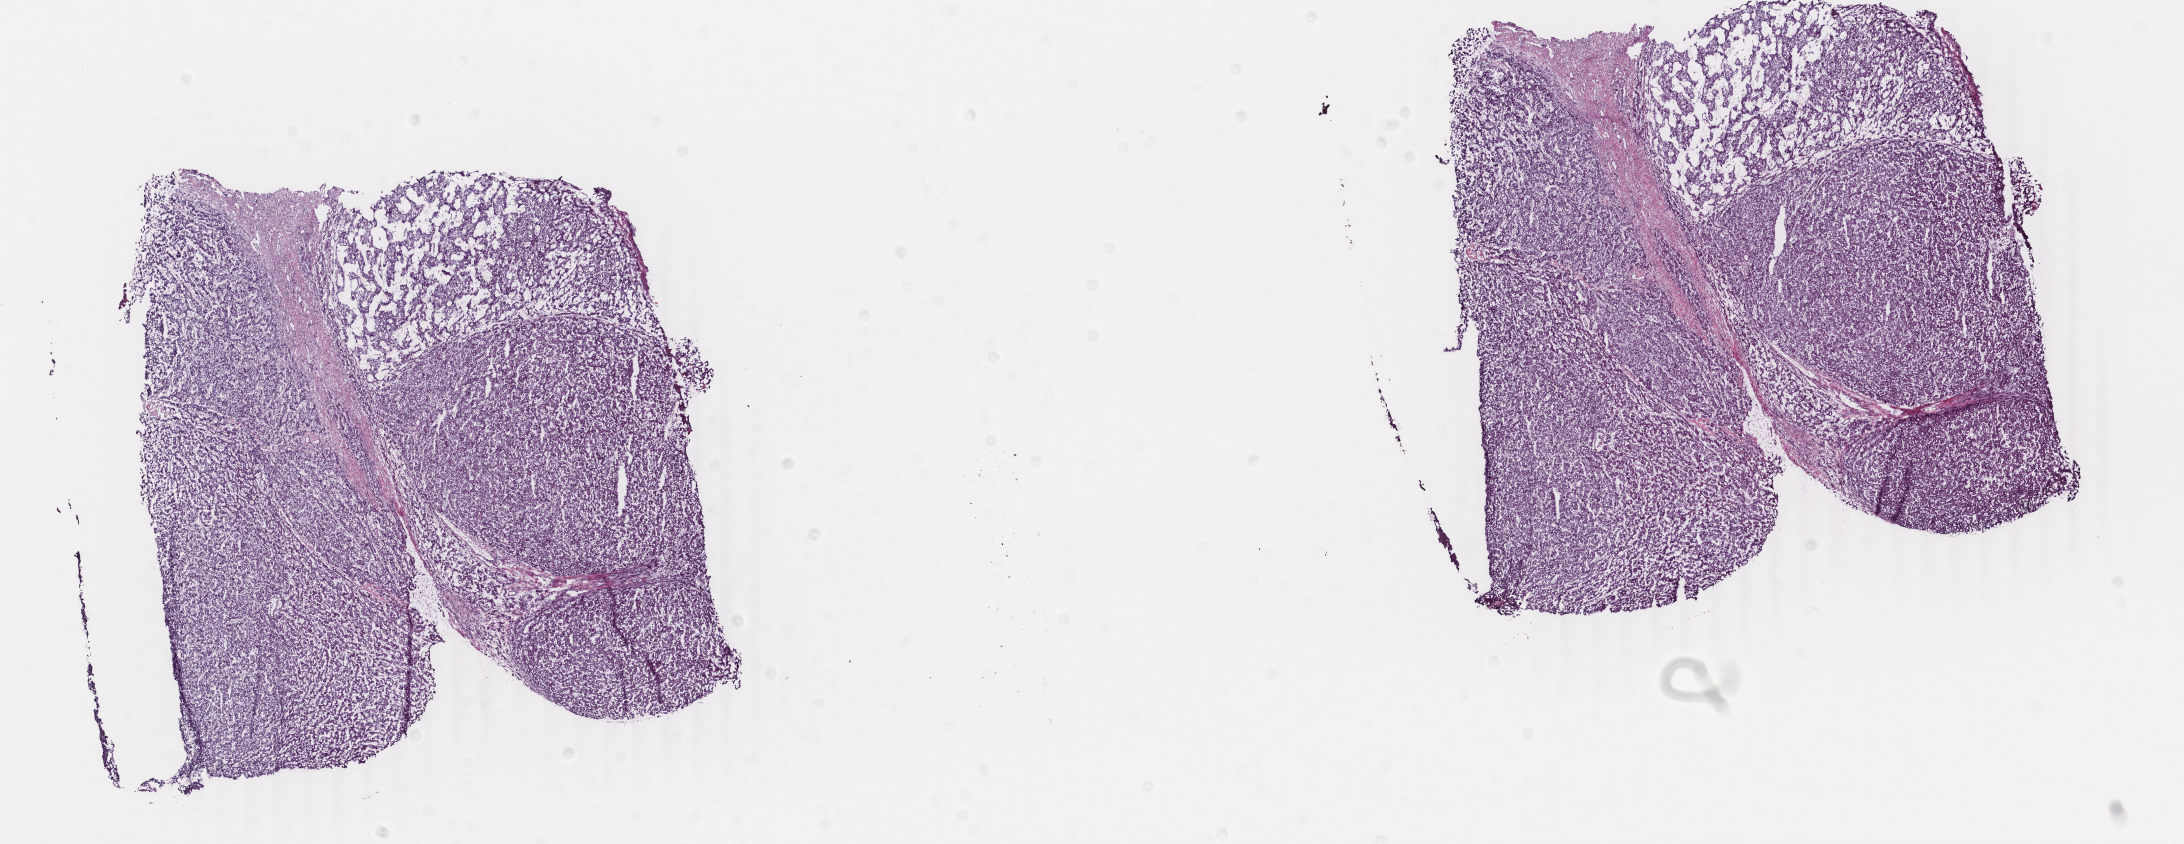
Digitized H&E-stained tissue section (whole slide), low-resolution overview of the scanned area, about 17.4 x 6.7 mm (from a 40x scan); frozen section from the bottom of the tissue portion; liver, primary tumour sample. Male patient; age at initial diagnosis 76 years. Histologic grade: G1 (well differentiated). Composition of this section per pathologist review: tumour cells 90%, tumour nuclei 95%, normal cells 0%, stromal cells 10%, necrosis 0%. Infiltration values recorded for this section: lymphocyte infiltration 0%, monocyte infiltration 0%, neutrophil infiltration 0%.
• pathologic diagnosis: Hepatocellular carcinoma, NOS